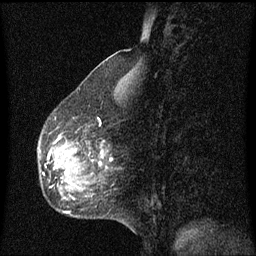
Breast MRI (dynamic contrast-enhanced), one sagittal slice. Slice 26 of 60 in the series (ordered by position). Dynamic contrast-enhanced series, image 2 of 3 at this slice position (ordered by acquisition). 1.5 T. TE 4.2 ms, TR 8.4 ms. 256 × 256 image matrix, field of view 200 × 200 mm. Patient: female, 49 years. From the clinical record (not read from this slice): setting: breast cancer imaged before/during neoadjuvant chemotherapy; receptor status: HR-positive, HER2-negative.
Annotated regions visible in this slice (semi-automatically segmented with operator editing):
- analysis volume of interest (the breast-tissue region the enhancement analysis was run in; not a lesion): bounding box <39,134,104,201> (left, top, right, bottom; pixels)
- tumour enhancement mask (voxels above the 70 % enhancement threshold inside the analysis volume of interest): <66,152,71,175>